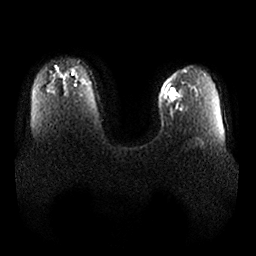
Breast MRI, one axial slice. Diffusion-weighted series; image 2 of 4 stored at this slice position (different b-values; order by instance number). 1.5 T. 4 mm slice thickness. 256 × 256 image matrix, field of view 380 × 380 mm. Female patient.
Outlined on this slice (outlined manually by an expert reader):
- tumour on diffusion-weighted imaging: bounding box <166,85,179,101> (left, top, right, bottom; pixels)